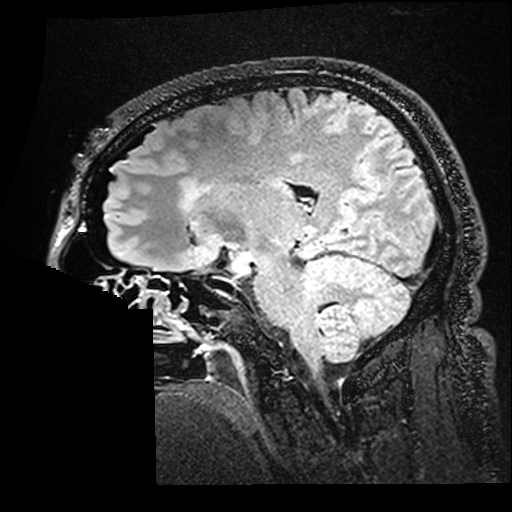
Brain MRI from a brain-tumour surgery series, one sagittal slice. Slice 105 of 176 in the series (ordered by position). T2 FLAIR. 1 mm slice thickness. 512 × 512 image matrix, field of view 250 × 250 mm. Case-level facts recorded for this patient, not image findings: histopathology: Astrocytoma; WHO grade: 2; IDH mutation: yes.
Outlined on this slice (expert manual segmentation):
- residual tumour: bounding box [x1, y1, x2, y2] px = [185, 186, 203, 206]